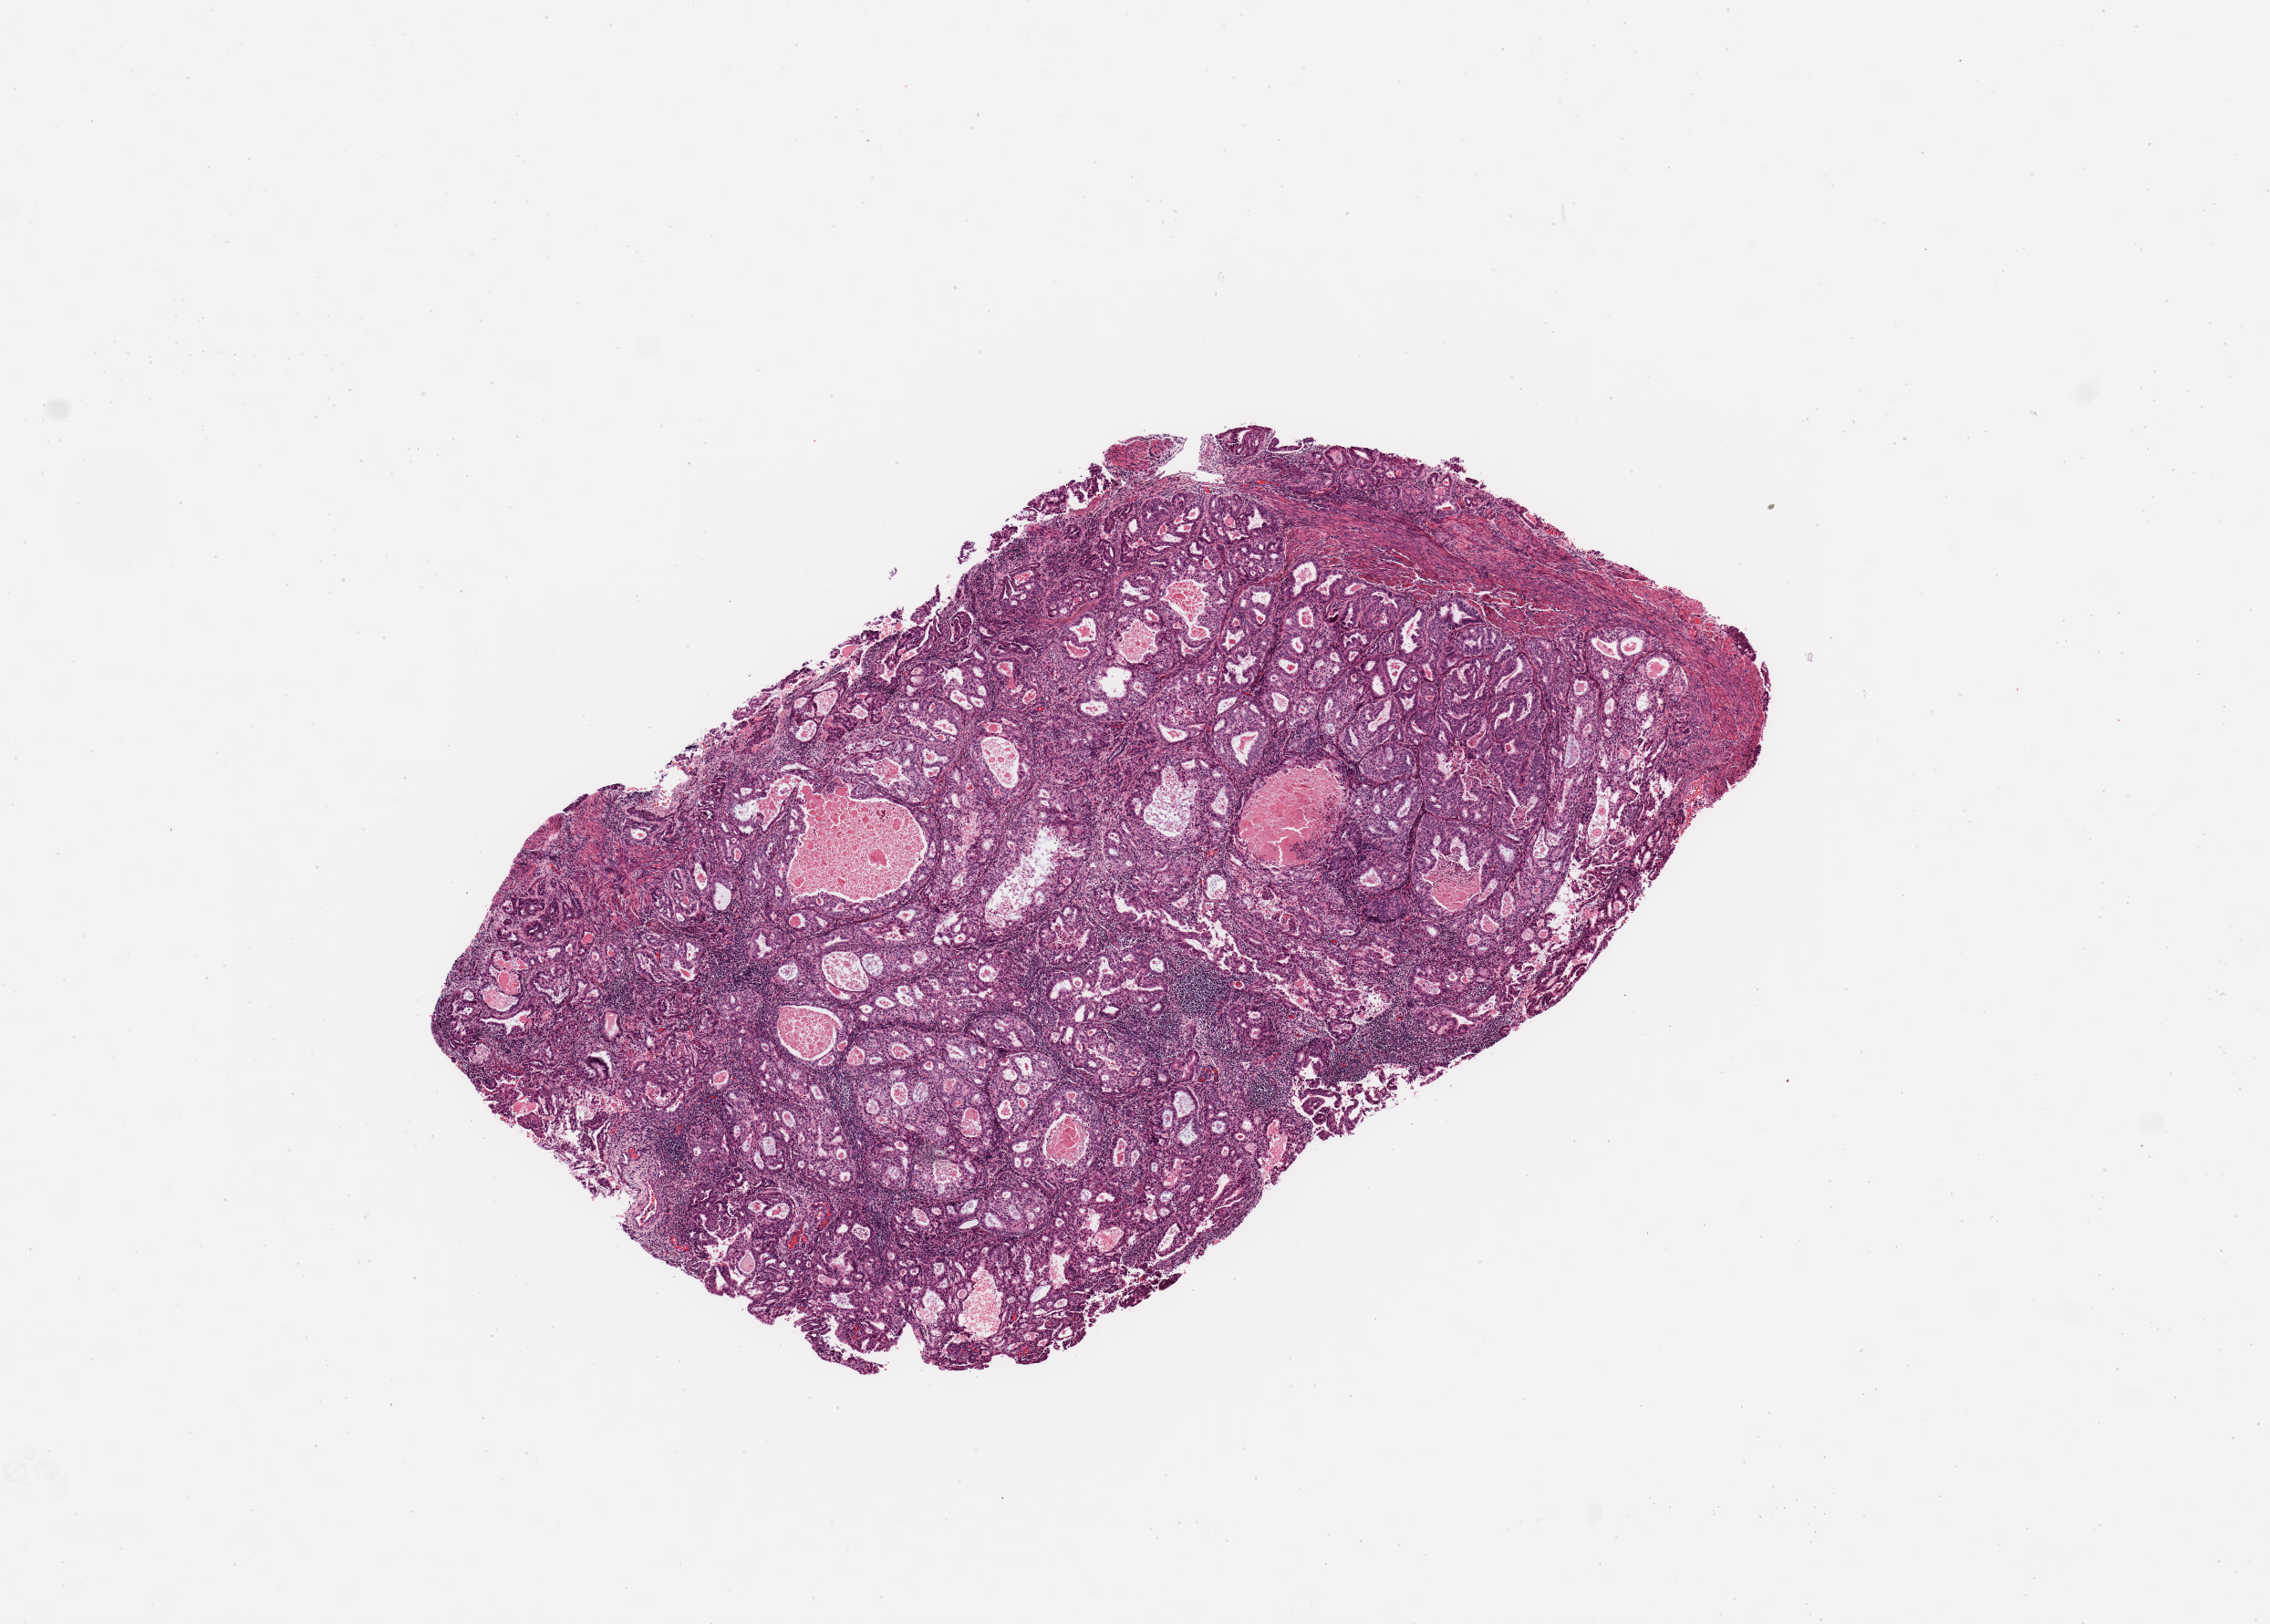
Digitized H&E-stained tissue section (whole slide), shown as a low-resolution overview of the whole scanned area (about 9.8 x 7.0 mm, from a 20x scan). Tumour tissue sample, sampled site: uterus. Female, 66 y/o. Composition of this section per pathologist review: tumour nuclei 90%, necrosis 5%.
Histologic diagnosis: Endometrioid adenocarcinoma, NOS. AJCC pathologic stage: II.